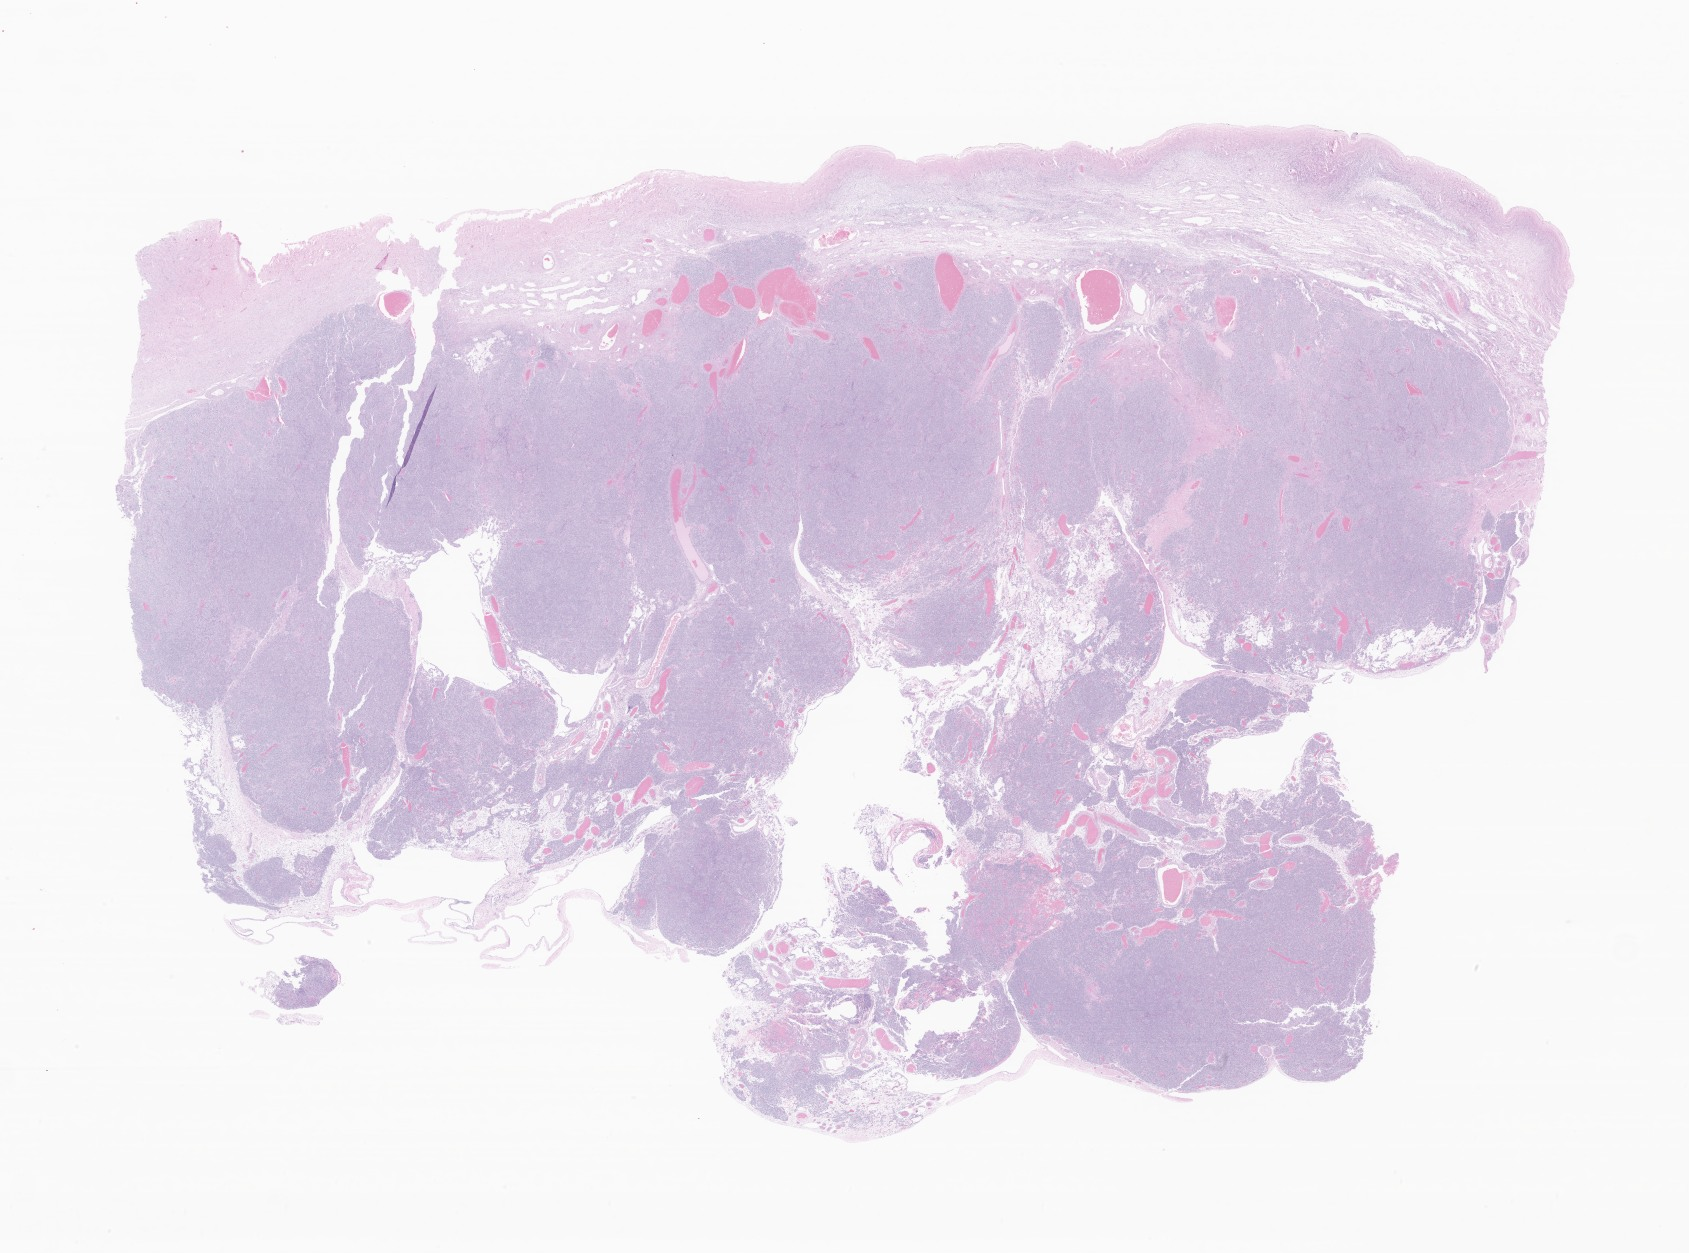
H&E whole-slide image of tumor tissue from the ovary — whole scanned area (about 28.5 x 21.1 mm) shown as a low-resolution overview; formalin-fixed, paraffin-embedded (FFPE) tissue. Patient: female, age 199 months (16 years 7 months).
* diagnosis: Sex cord-gonadal stromal tumor, NOS